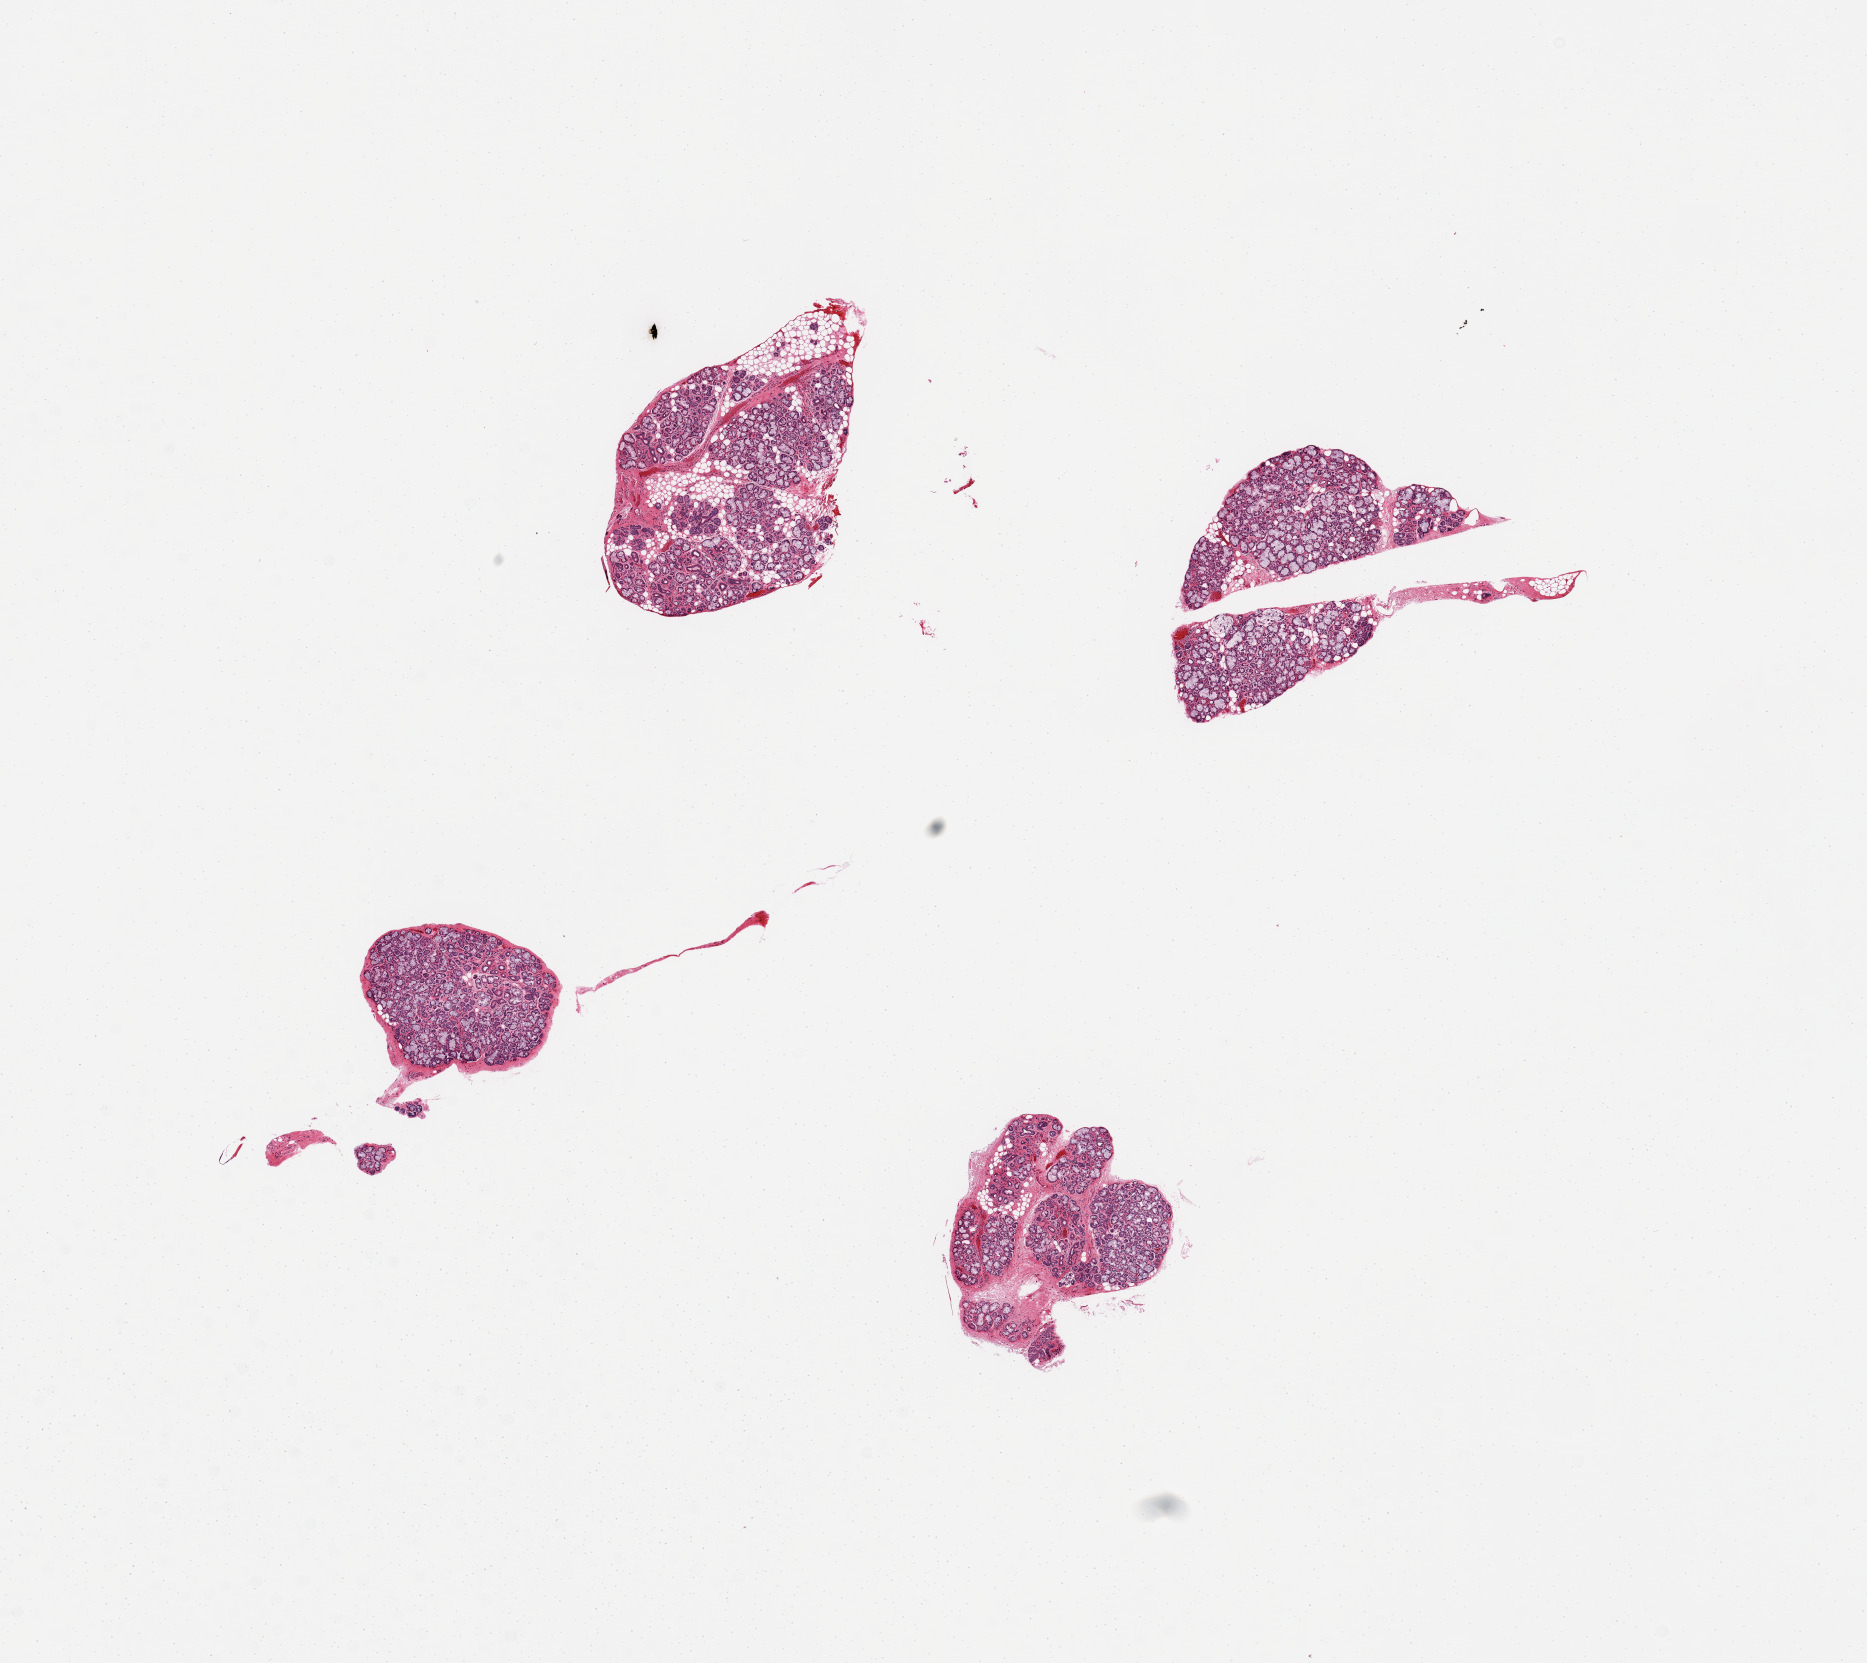
Hematoxylin and eosin (H&E) whole-slide image — whole scanned area (about 14.8 x 13.2 mm, acquisition: 20x scan) shown as a low-resolution overview; PAXgene-fixed, paraffin-embedded tissue; section of minor salivary gland (target tissue); tissue donor sample. Donor sex: male.
Reviewer comment on this tissue sample: 4 pieces, excellent specimen with small portion of fat/stroma.